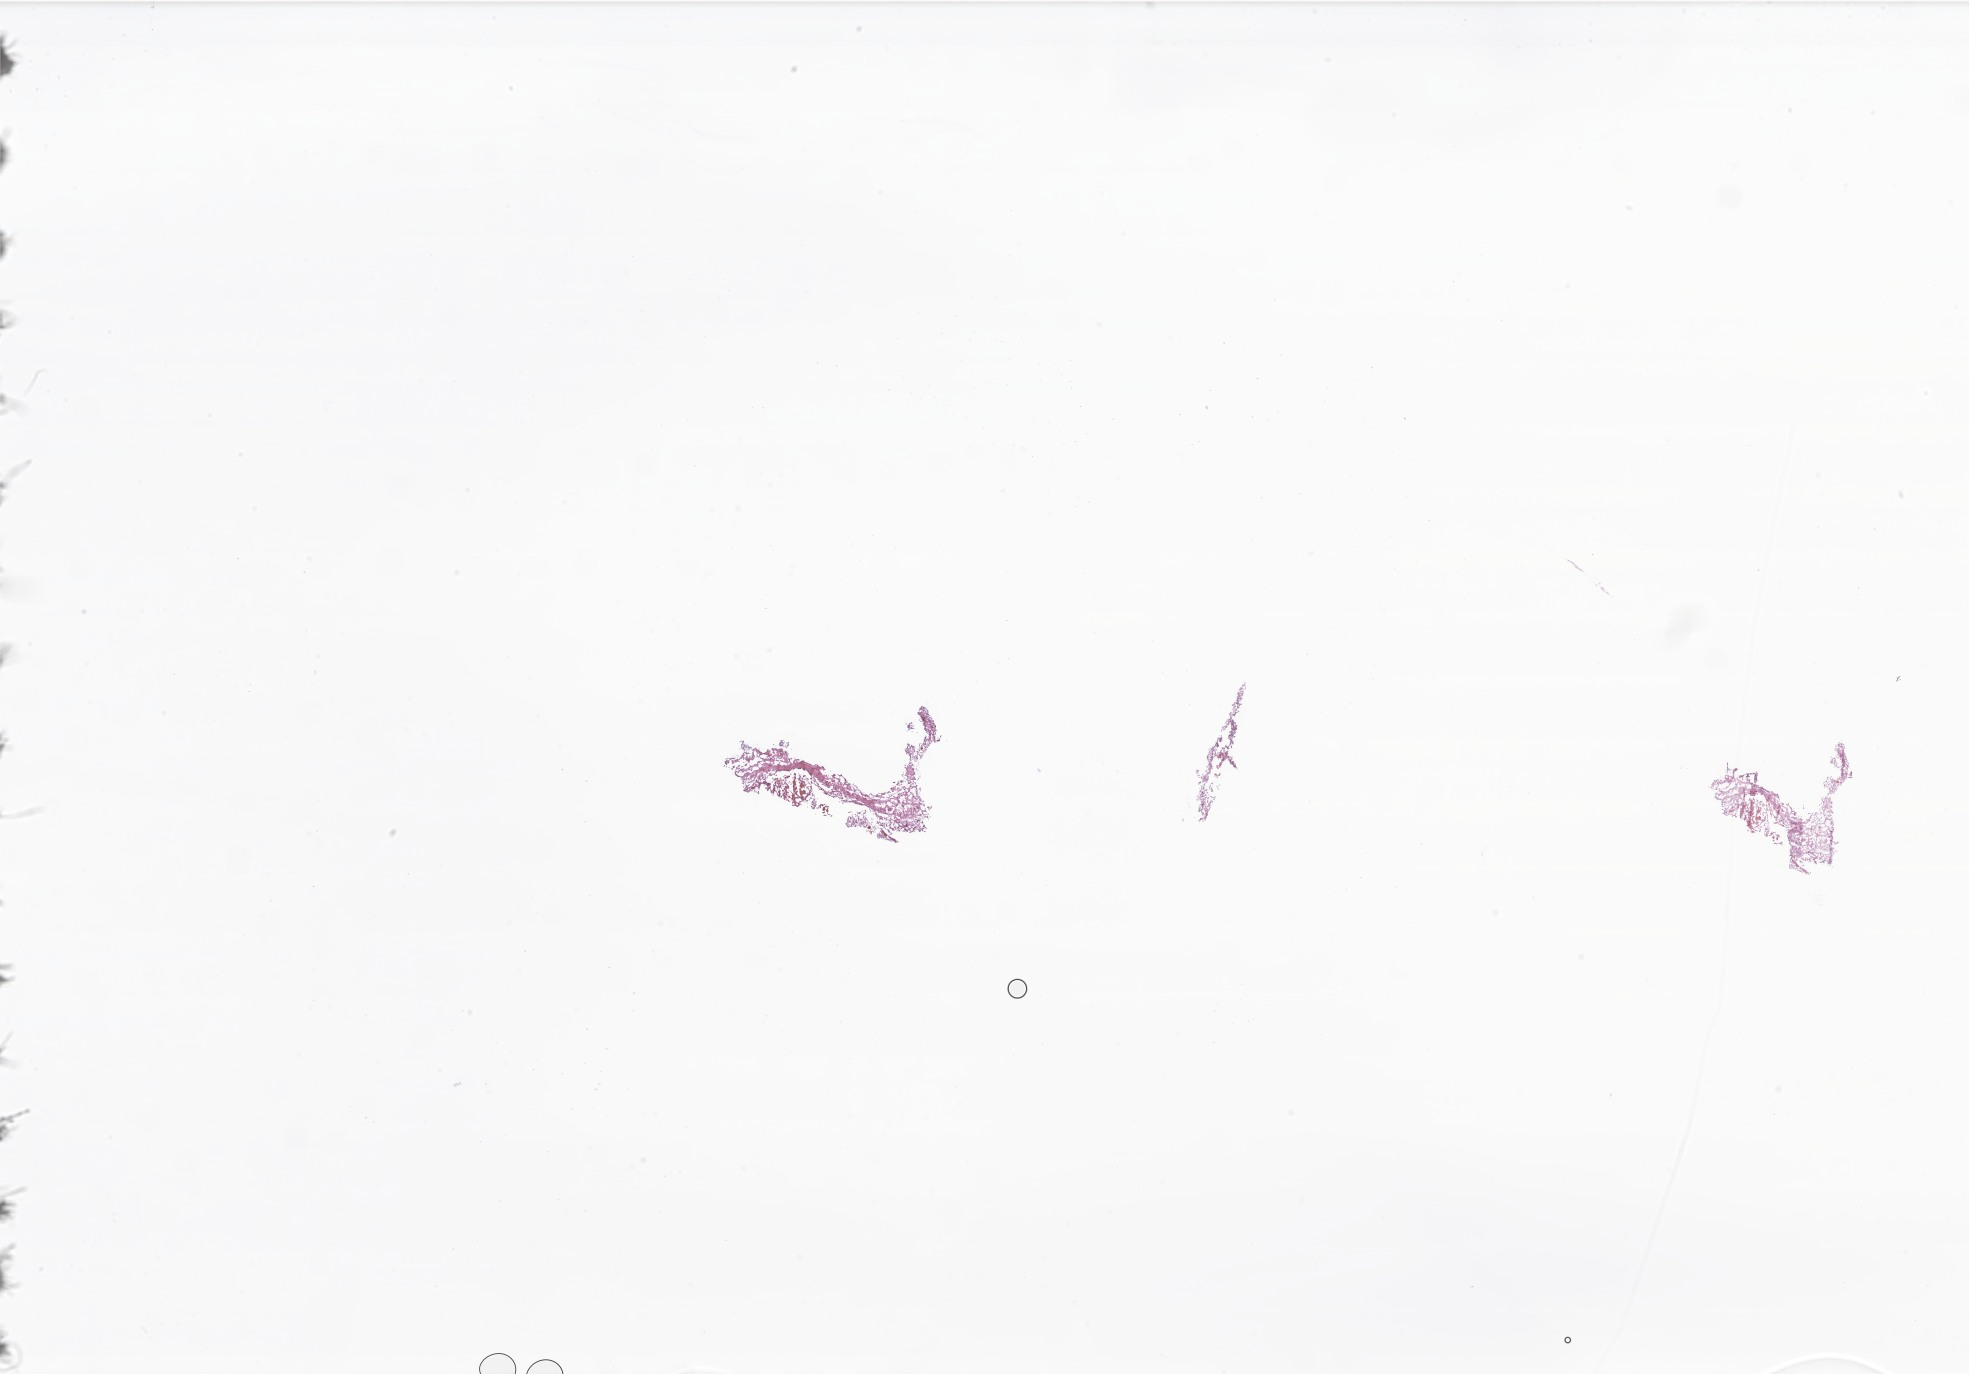
Digitized hematoxylin and eosin (H&E)-stained section of tumor tissue from the cerebellum — whole scanned area (about 33.2 x 23.2 mm) shown as a low-resolution overview. Frozen section (OCT-embedded). Patient: male, age 475 days (about 1.3 years).
Diagnosis (ICD-O-3 morphology term): Pilocytic astrocytoma.